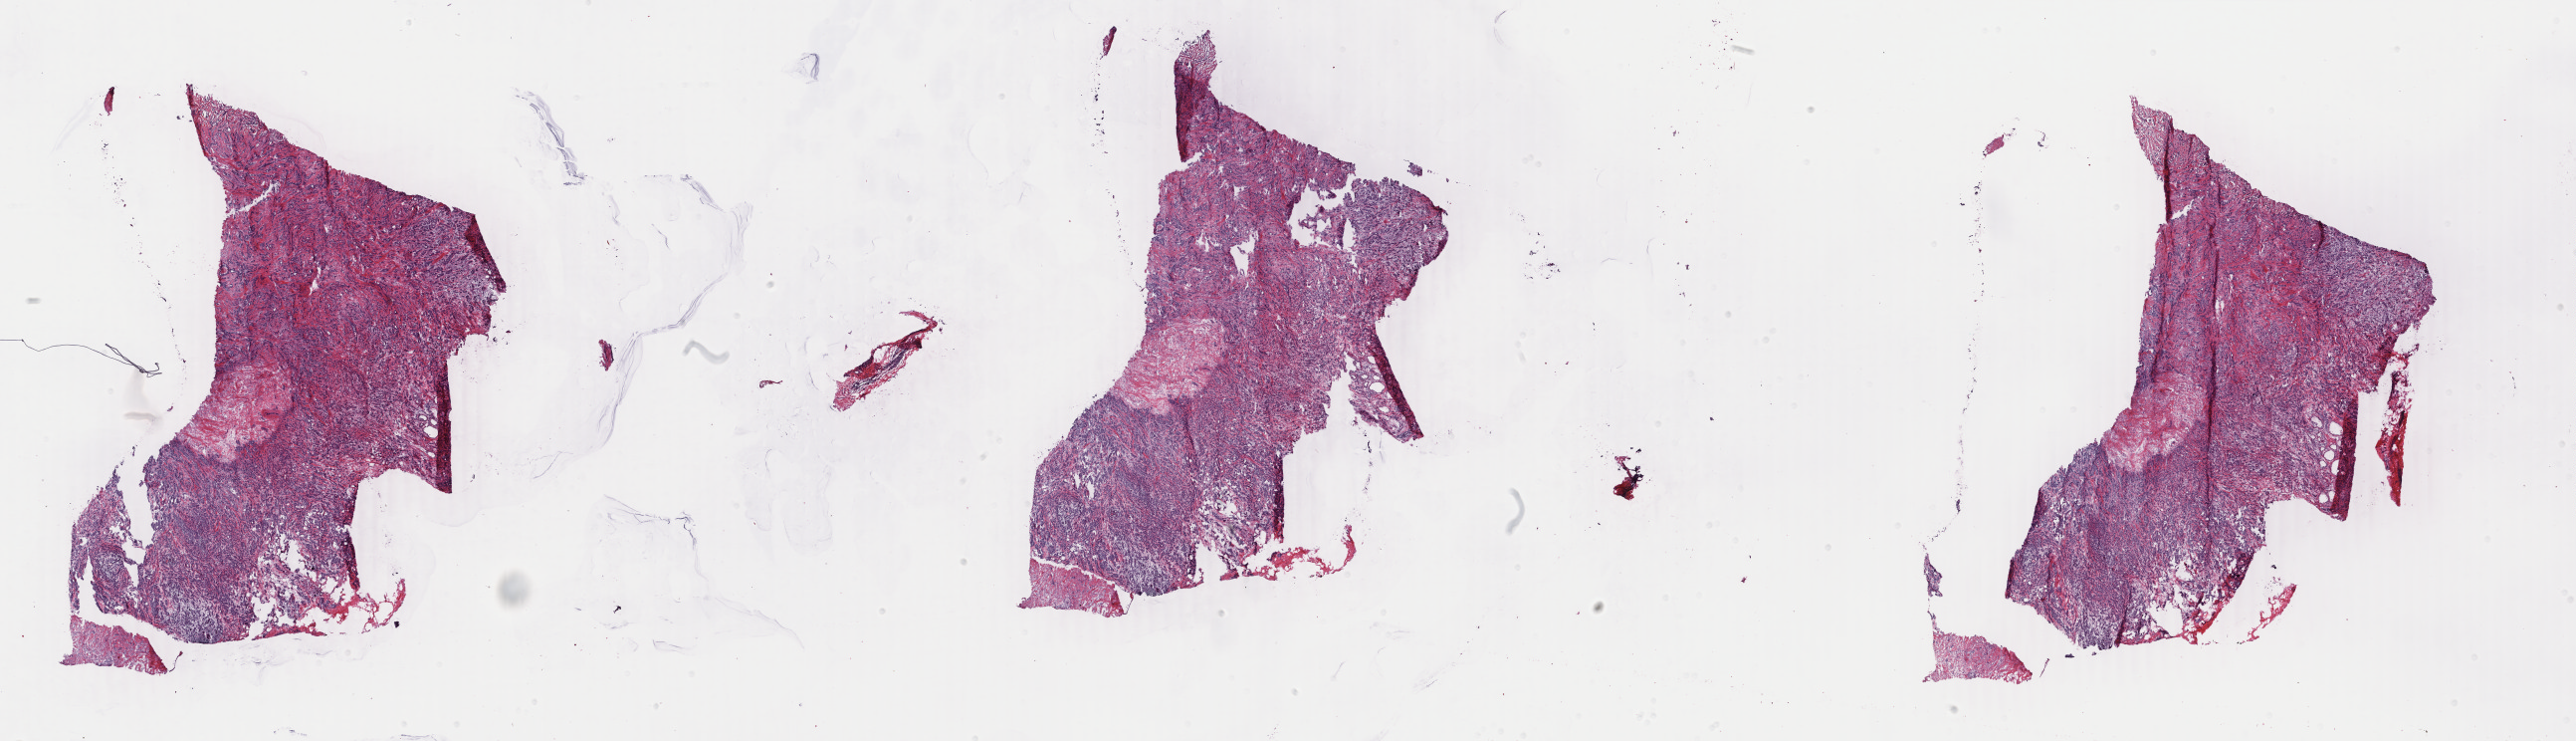
H&E whole-slide image, a low-resolution overview of the entire scanned area, about 41.2 x 11.8 mm (acquisition: 40x scan); frozen section from the bottom of the tissue portion; primary tumour sample from the breast. Female, age 56 years at initial diagnosis. Composition of this section per pathologist review: tumour cells 85%, tumour nuclei 90%, normal cells 0%, stromal cells 14%, necrosis 1%. Inflammatory infiltration, as recorded: lymphocyte infiltration 1%, monocyte infiltration 0%, neutrophil infiltration 0%.
AJCC pathologic stage: IIA. TNM: T2 N0 (i-) M0. Diagnosis: Infiltrating duct carcinoma, NOS. Laterality: right.